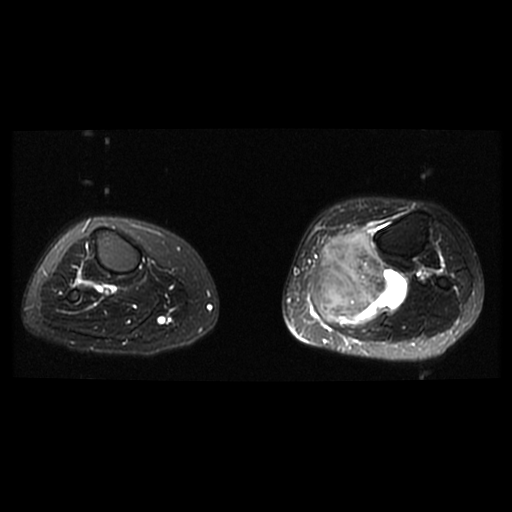
MRI of an extremity soft-tissue mass, one axial slice; T2-weighted fat-saturated; 512 × 512 image matrix, field of view 330 × 330 mm. Female patient. From the clinical record (not read from this slice): histological type: extraskeletal high grade osteogenic sarcoma; grade: high; site of the primary tumour: left calf.
Annotated regions visible in this slice (expert manual segmentation):
- gross tumour volume (mass): bounding box [x1, y1, x2, y2] px = [312, 230, 409, 323]